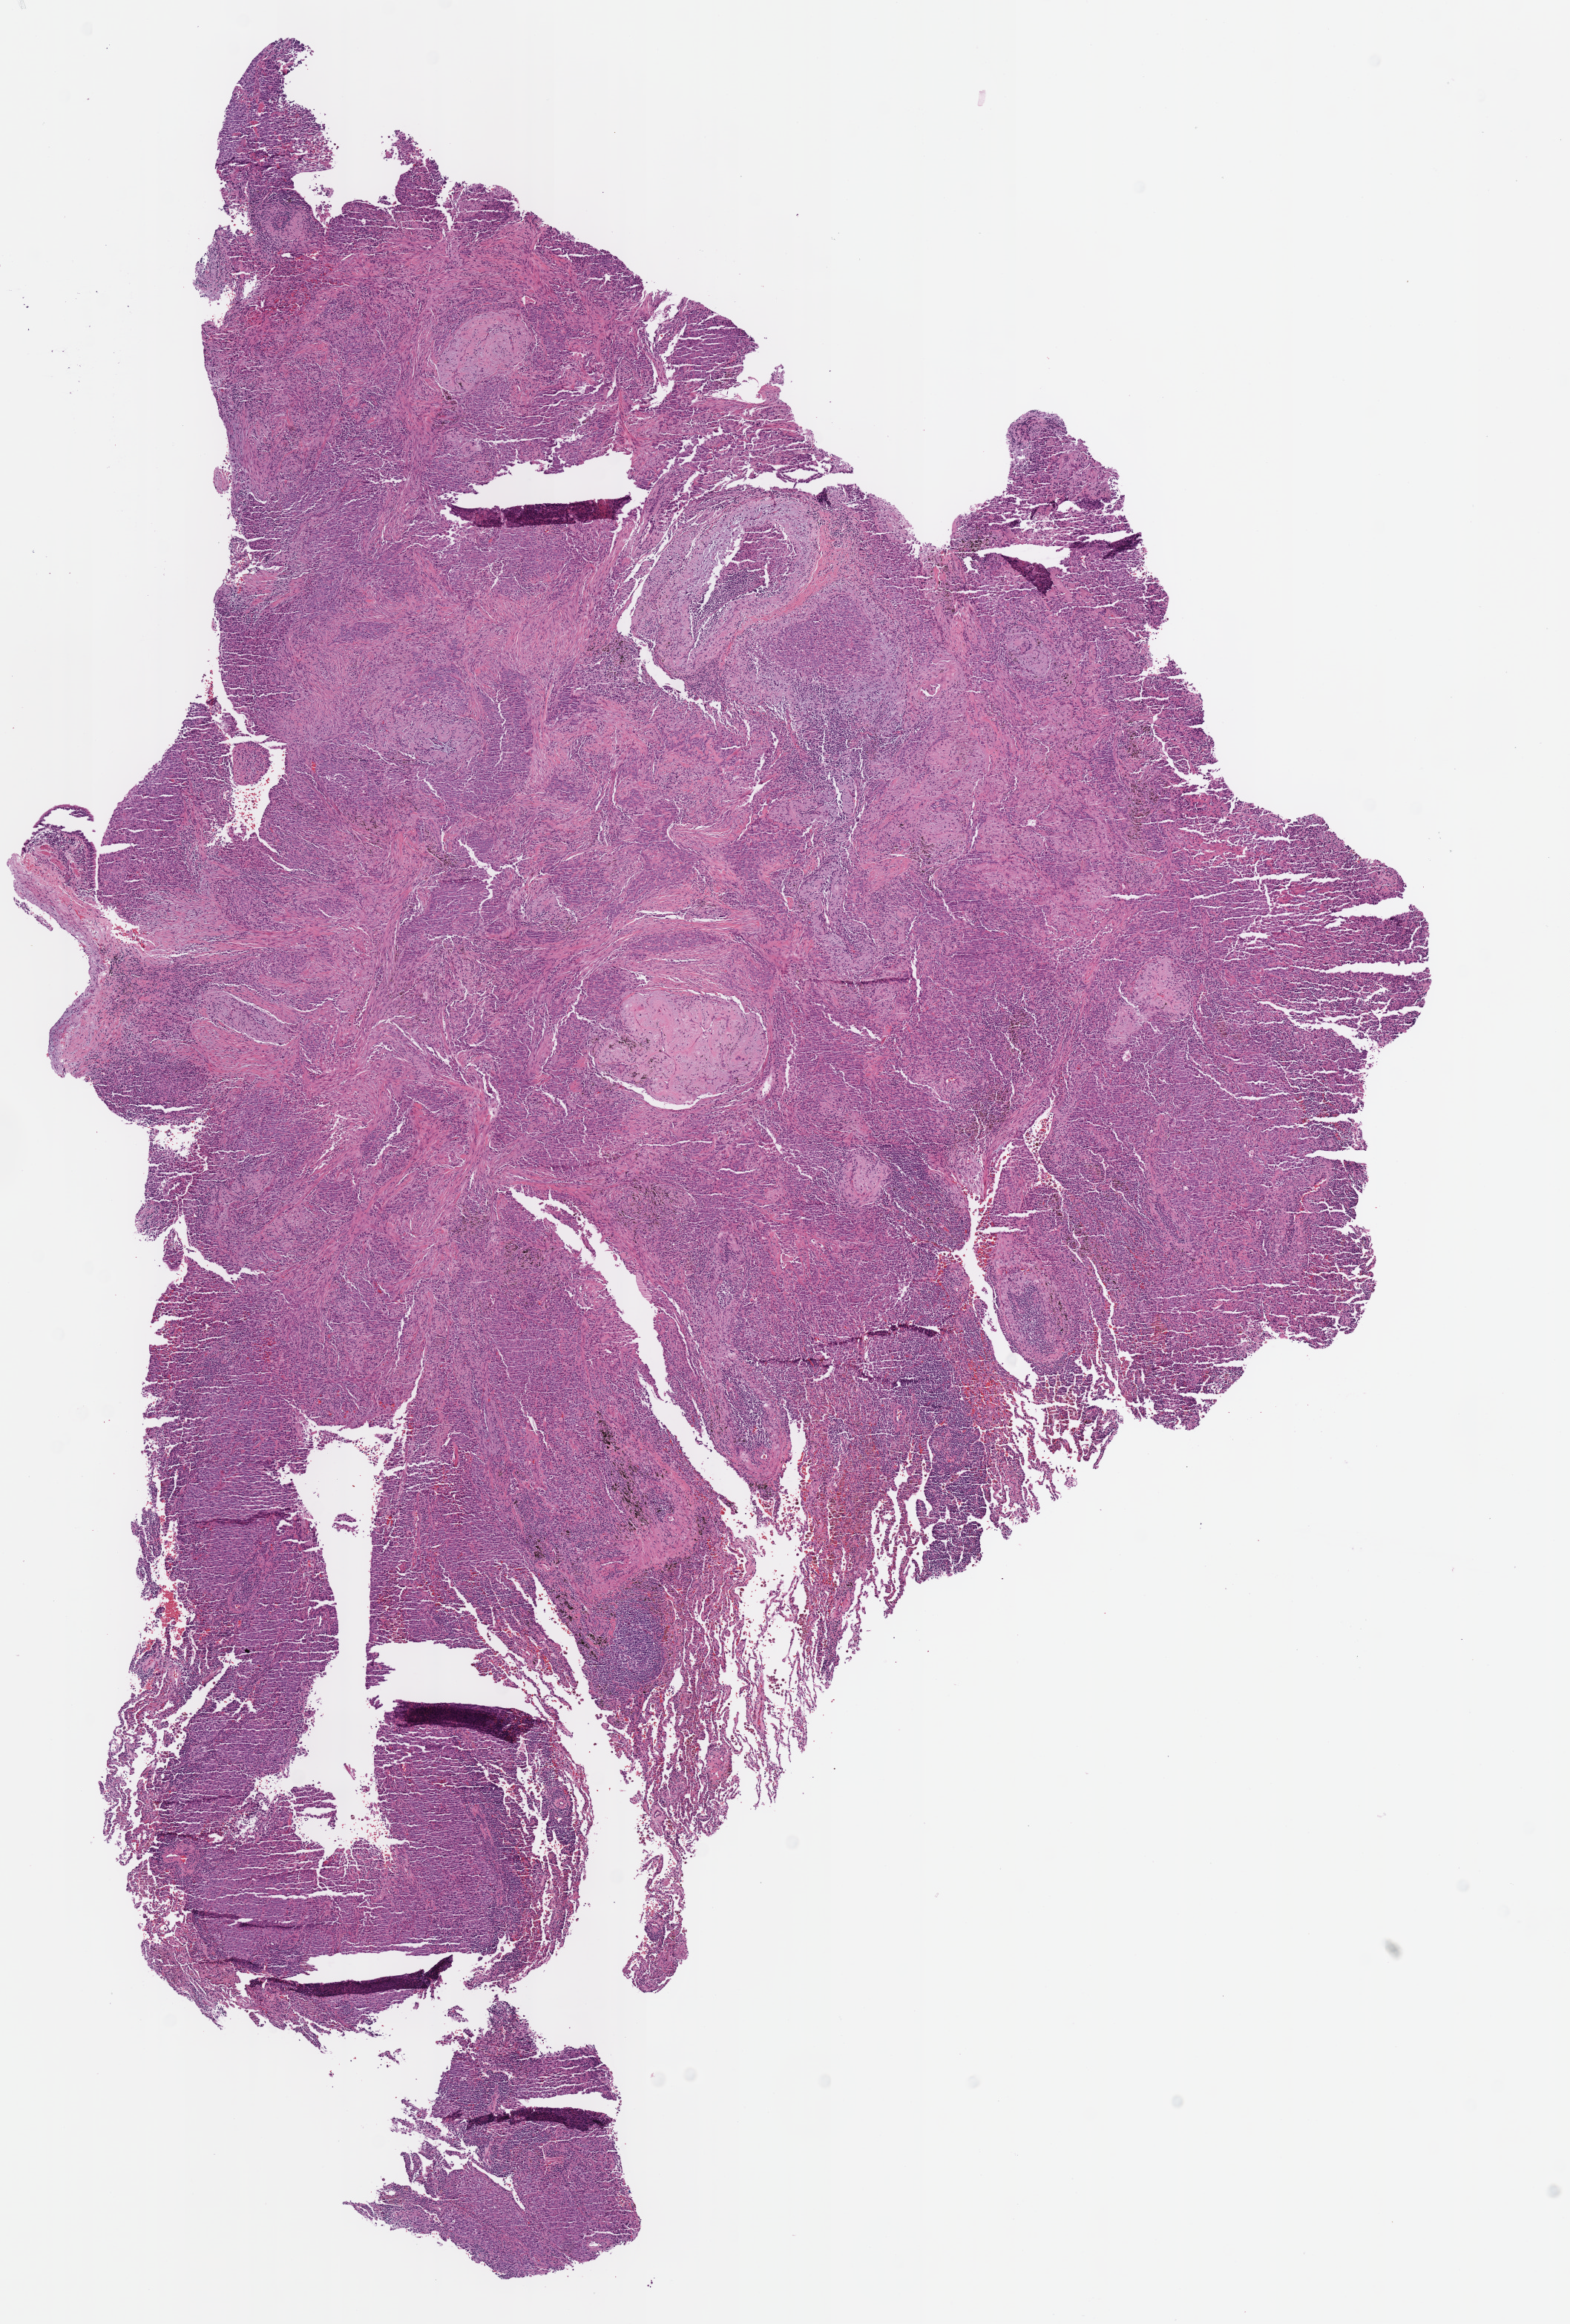
Hematoxylin and eosin (H&E) stained whole-slide image — whole scanned area (about 8.3 x 12.3 mm) shown as a low-resolution overview; formalin-fixed paraffin-embedded (FFPE) diagnostic section; sample: primary tumour, lung. Patient: male, age at initial diagnosis 66 years.
Pathologic diagnosis: Squamous cell carcinoma, NOS (lower lobe, lung). AJCC pathologic stage: IA. Laterality: right. TNM: T1b N0 MX.